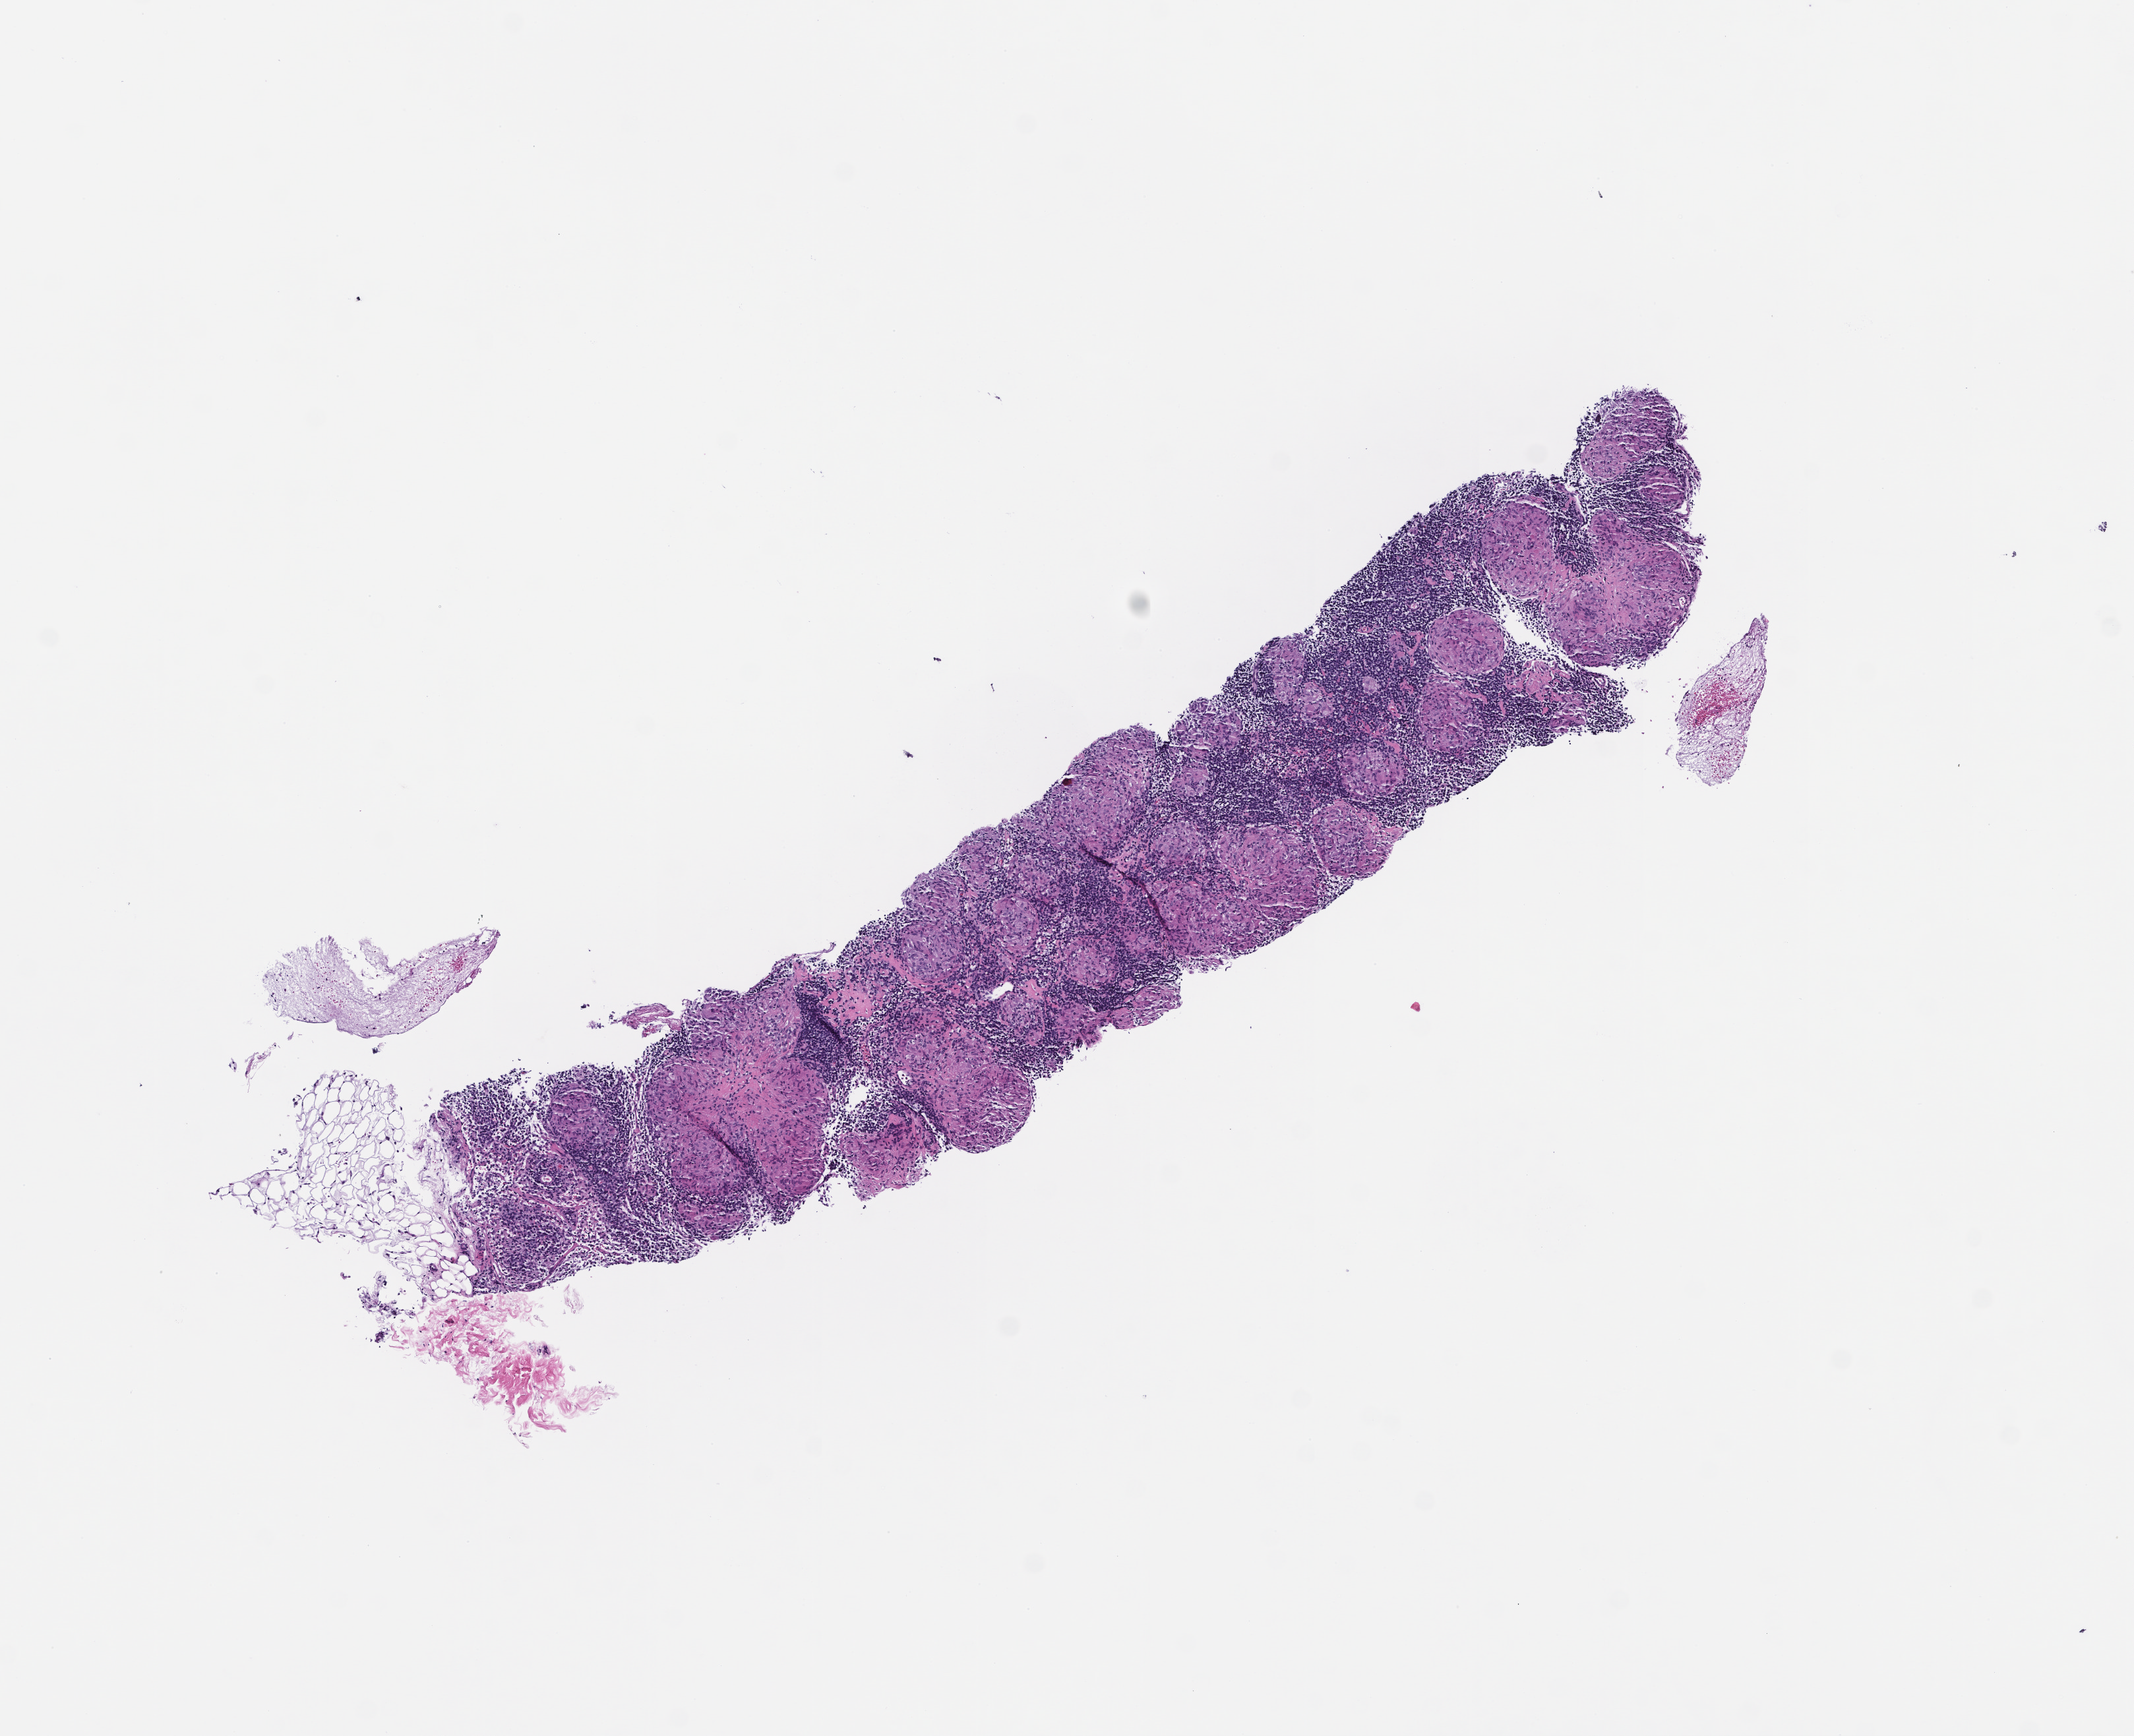
H&E whole-slide image — a low-resolution overview of the entire scanned area, about 6.5 x 5.3 mm, FFPE section. Male patient.
* this section: metastatic tumor tissue
* patient diagnosis (primary): Non-Small Cell Lung Carcinoma